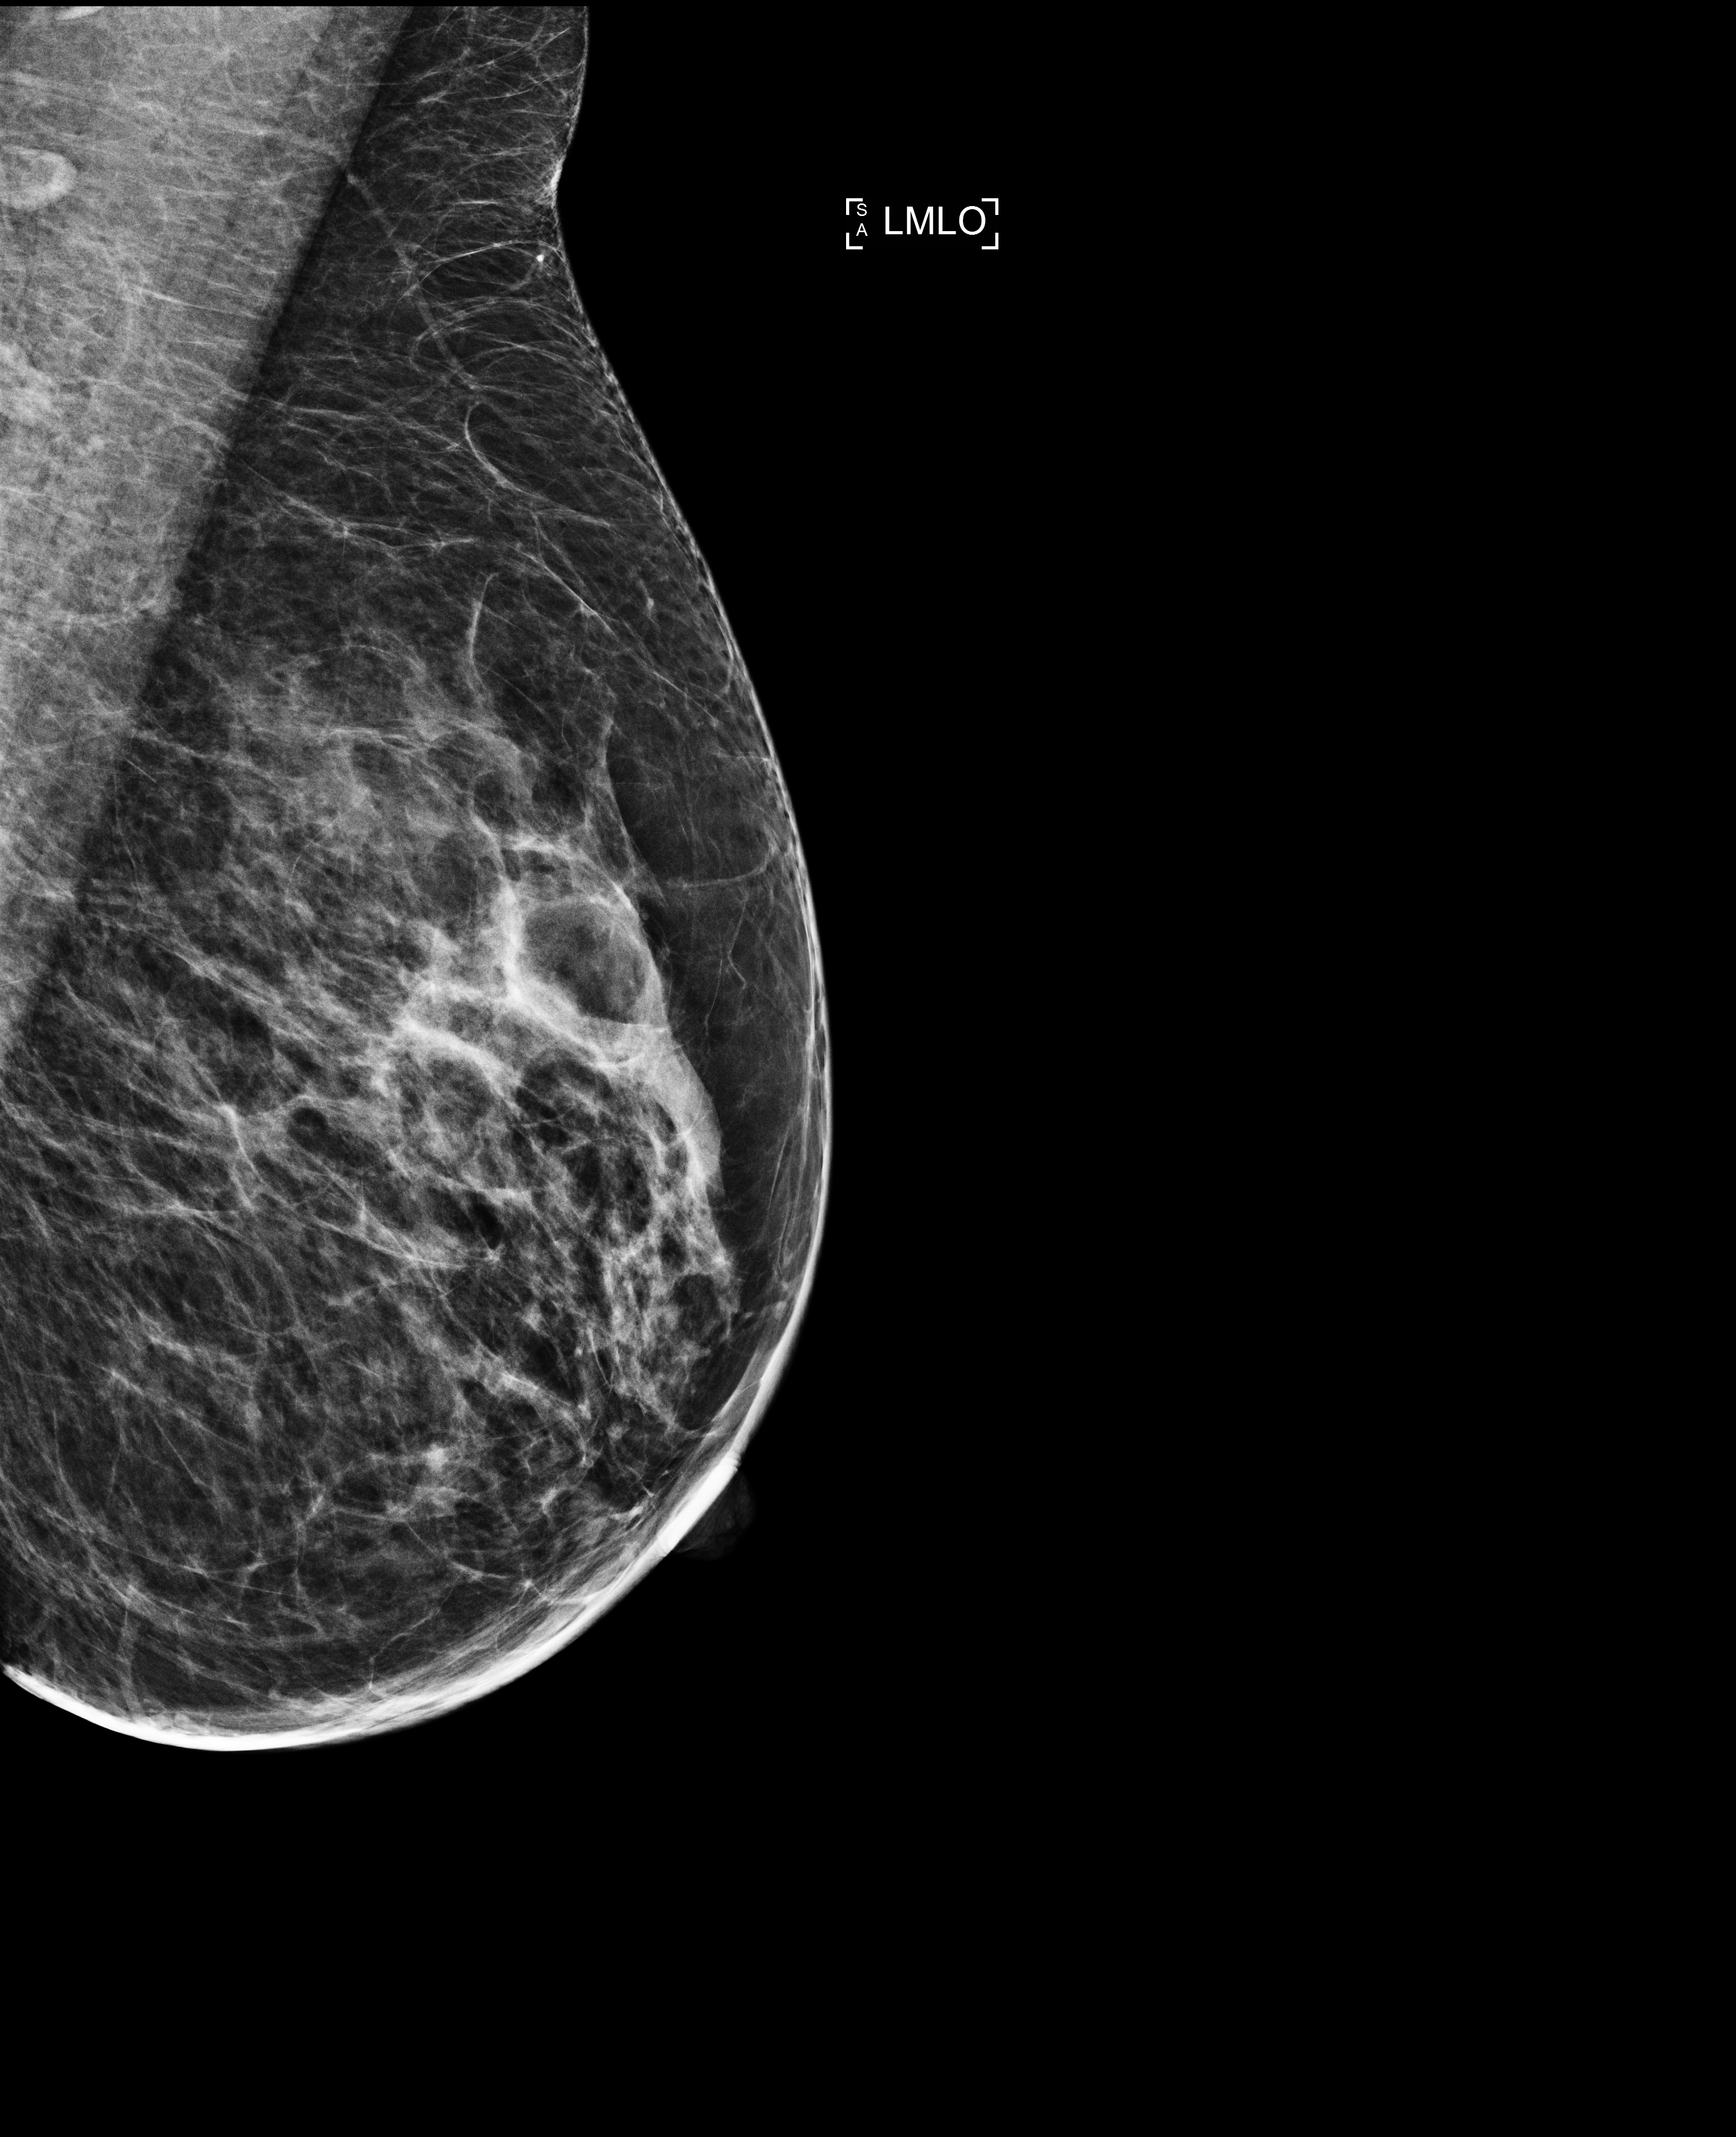
Digital mammogram (FFDM); left breast; MLO view; annual screening mammography examination; compressed breast thickness 46 mm; system: Selenia Dimensions. Female patient, age 56 years.
Final BI-RADS assessment for this screening round (tomosynthesis exam, both breasts): category 1.